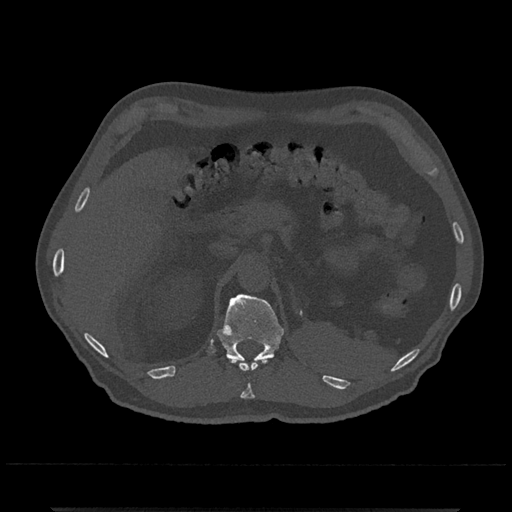
CT including the spine, one axial slice; slice 450 of 797 in the series (ordered by position); reconstruction kernel Br40s/3; bone window (W 1800 / L 400 HU); 0.5 mm slice thickness; 512 × 512 image matrix, field of view 393 × 393 mm. Male patient, age 67 years. Case-level facts recorded for this patient, not image findings: primary cancer: prostate.
Annotated regions visible in this slice (semi-automatic segmentation, software-assisted and operator-edited):
- T11 vertebra: bounding box [x1, y1, x2, y2] px = [230, 358, 267, 399]
- T12 vertebra: [217, 294, 284, 363]